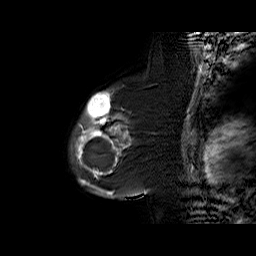
Breast MRI (dynamic contrast-enhanced), one sagittal slice. Slice 46 of 60 in the series (ordered by position). Dynamic contrast-enhanced series, time point 2 of 6 at this slice position (early post-contrast). 1.5 T. TE 6.3 ms, TR 32.4 ms. 256 × 256 image matrix, field of view 200 × 200 mm. Female patient. From the clinical record (not read from this slice): setting: breast cancer imaged before/during neoadjuvant chemotherapy; receptor status: triple-negative.
Outlined on this slice (semi-automatic segmentation, software-assisted and operator-edited):
- analysis volume of interest (the breast-tissue region the enhancement analysis was run in; not a lesion): bounding box (x1, y1, x2, y2) in pixels: (69, 89, 136, 187)
- tumour enhancement mask (voxels above the 100 % enhancement threshold inside the analysis volume of interest): (74, 91, 128, 187)